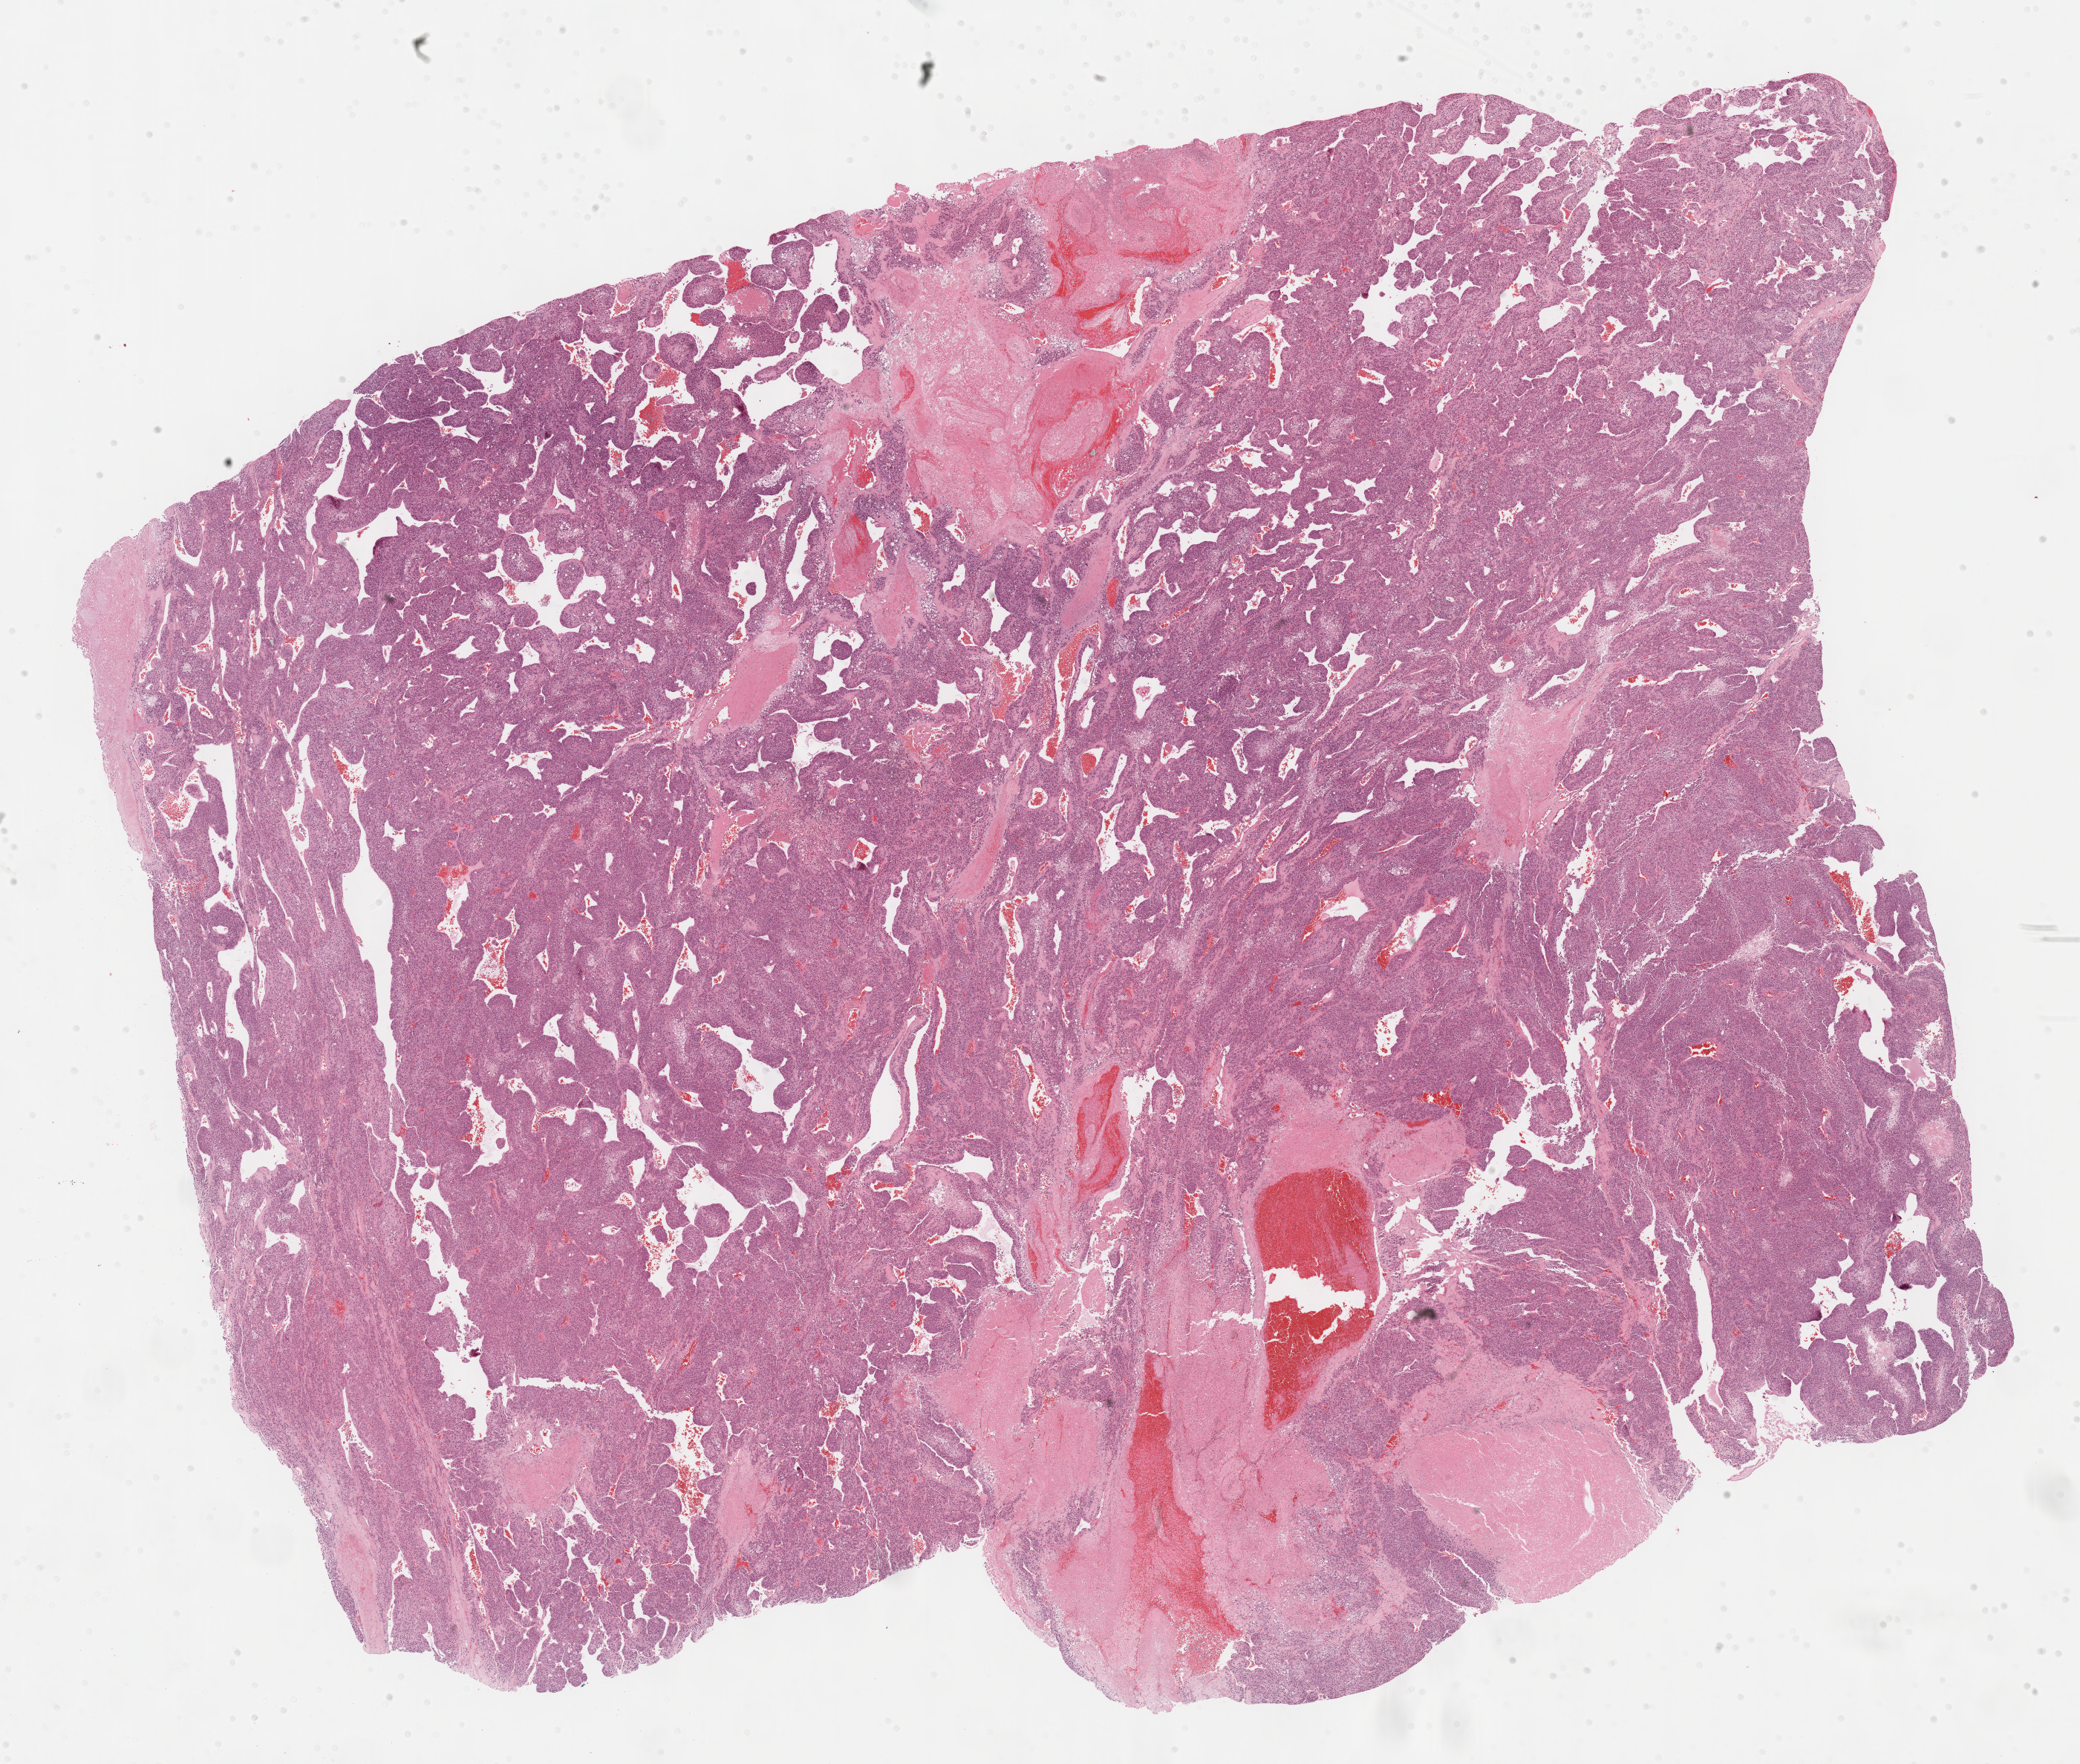
Digitized Hematoxylin and eosin (H&E) stained tissue section (whole slide) — low-resolution overview of the scanned area, about 22.7 x 19.2 mm (slide scanned at 40x); FFPE section; sample: primary tumour, adrenal cortex. Patient: female, age at initial diagnosis 59 years.
* lymph nodes positive (case pathology): 0 of 20 examined
* laterality: left
* diagnosis: Adrenal cortical carcinoma (cortex of adrenal gland)